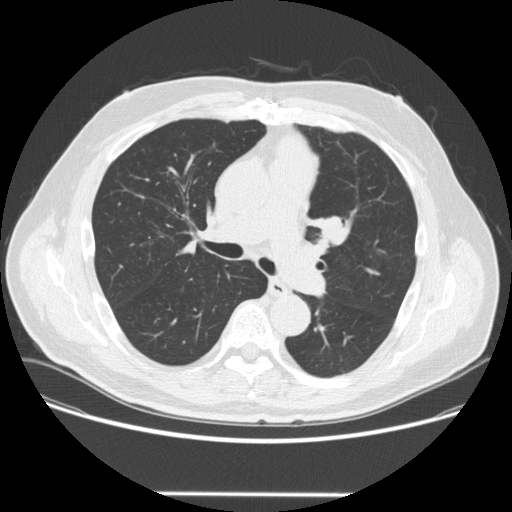
Low-dose screening chest CT, one axial slice; slice 162 of 253 in the series (ordered by position); reconstruction kernel STANDARD; 120 kVp; lung window (W 1500 / L -600 HU); 2.5 mm slice thickness; 512 × 512 image matrix.
Annotated regions visible in this slice (manually delineated by an expert):
- lesion 1 (tumor, upper lobe of left lung): bounding box (x1, y1, x2, y2) in pixels: (317, 217, 343, 243)